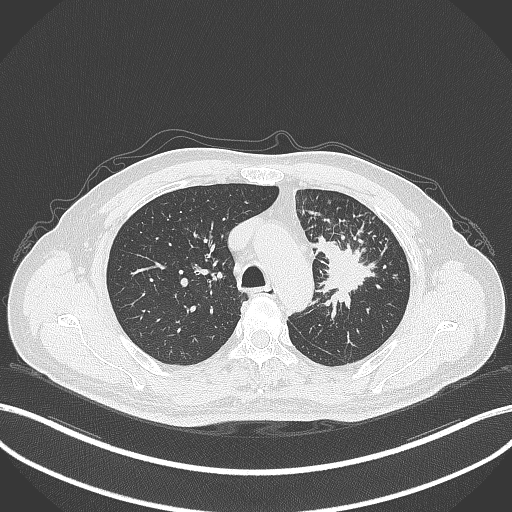
Chest CT, one axial slice; position 262 of 386 along the scan axis; reconstruction kernel B70f; 120 kVp; lung window (W 1500 / L -600 HU); 1 mm slice thickness; 512 × 512 image matrix. Male patient, age 69 years. From the clinical record (not read from this slice): clinical TNM (as recorded): T2a N2 M0.
Structures marked on this image (rectangle marked by the reading radiologist):
- lung tumour (recorded histology: adenocarcinoma): box from (x=310, y=234) to (x=381, y=318) px